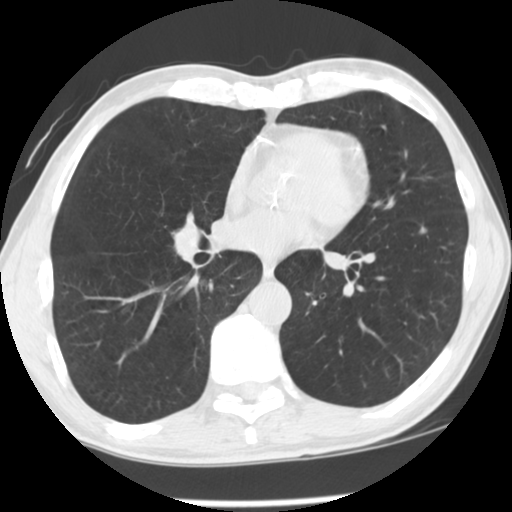
Low-dose screening chest CT, axial slice. Third screening round (two years after baseline). Lung window (W 1500 / L -600 HU). Slice 77 of 139 in the series. Male, age 63 years at enrolment. Current smoker at enrolment.
Expert-annotated lung lesion, box from (x=406, y=220) to (x=440, y=245) px. The exam's reader record, not a measurement of the box and not confirmed to be the same lesion: non-calcified nodule or mass ≥4 mm, left lower lobe, 6 × 5 mm, smooth margins, soft tissue attenuation, pre-existing on the prior screen: no. Later outcome: lung cancer diagnosed 269 days after this screen — squamous cell carcinoma, NOS, left lower lobe, poorly differentiated (G3), stage IA (AJCC 6th edition), 4 mm at pathology.